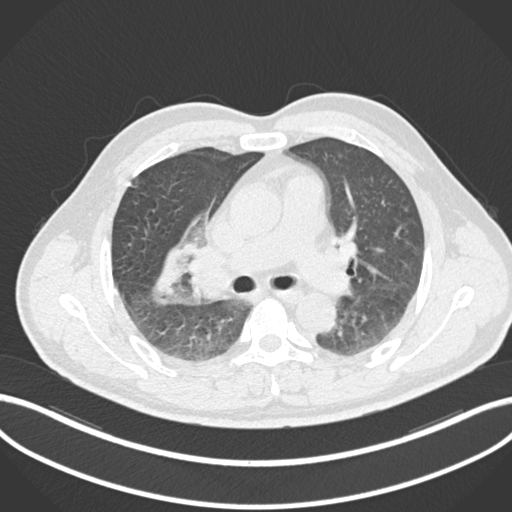
Chest CT, one axial slice; slice 637 of 852 in the series (ordered by position); reconstruction kernel B30f; lung window (W 1500 / L -600 HU); 512 × 512 image matrix, field of view 400 × 400 mm. Male patient, age 55 years. From the clinical record (not read from this slice): clinical TNM (as recorded): T3 N2 M1.
Structures marked on this image (bounding box drawn by a radiologist):
- lung tumour (recorded histology: adenocarcinoma): bounding box [x1, y1, x2, y2] px = [153, 241, 185, 308]